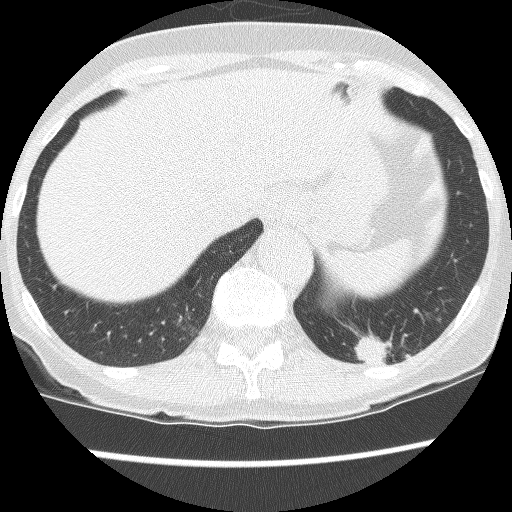
Axial slice from a low-dose chest CT screening exam. Third screening round (two years after baseline). Lung window (W 1500 / L -600 HU). 2.5 mm slice thickness. Lung (sharp) reconstruction kernel (BONE). 120 kVp. Female, age 61 years at enrolment. Current smoker at enrolment.
- Expert reader's lesion annotation, bounding box (x1, y1, x2, y2) in pixels: (336, 295, 439, 385).
- The screening reader recorded 2 non-calcified nodules or masses ≥4 mm on this exam (left lower lobe, left lower lobe); which of them this box marks is not recorded.
- Official screen result: positive, no significant change: stable abnormalities potentially related to lung cancer, unchanged since the prior screening exam.
- Lung cancer was diagnosed 166 days after this screen: non-small cell carcinoma, left lower lobe, poorly differentiated (G3), stage IB (AJCC 6th edition), 100 mm at pathology.